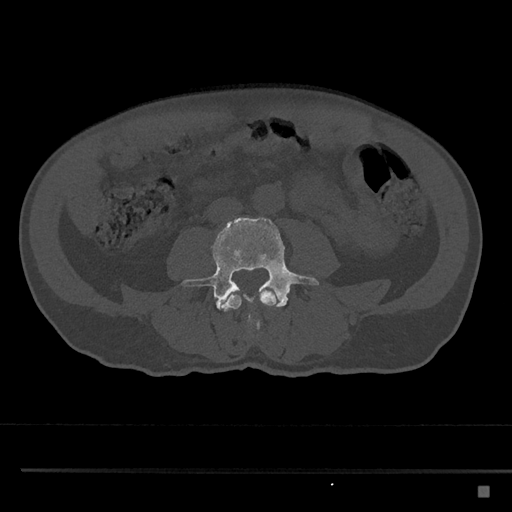
CT including the spine, one axial slice; slice 653 of 797 in the series (ordered by position); reconstruction kernel Br40s/3; 120 kVp; bone window (W 1800 / L 400 HU); 0.5 mm slice thickness; 512 × 512 image matrix, field of view 391 × 391 mm. Patient: male, 59 years. Case-level facts recorded for this patient, not image findings: primary cancer: prostate.
Outlined on this slice (semi-automatic segmentation, software-assisted and operator-edited):
- L3 vertebra: bounding box [x1, y1, x2, y2] px = [220, 289, 277, 330]
- L4 vertebra: [181, 217, 319, 329]